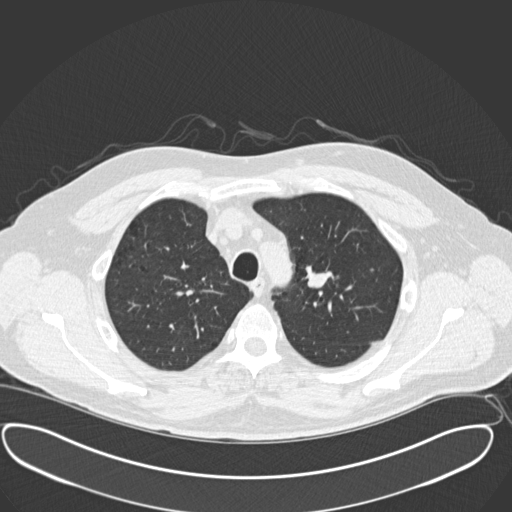
Axial slice from a low-dose chest CT screening exam; third screening round (two years after baseline); lung window (W 1500 / L -600 HU); standard (soft-tissue) reconstruction kernel (B30f); 512 × 512 image matrix. Male participant, aged 56 years at enrolment. Current smoker at enrolment.
Lesion marked by an expert reader, bounding box [x1, y1, x2, y2] px = [290, 262, 342, 309]. Screening reader's record for this exam: no non-calcified nodule ≥4 mm recorded. Participant outcome: lung cancer diagnosed 156 days after this screen — neuroendocrine carcinoma, NOS, left upper lobe, well differentiated (G1), stage IA (AJCC 6th edition), 20 mm at pathology.